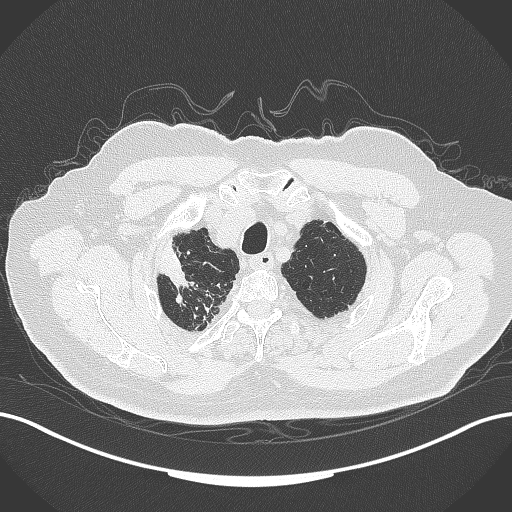
Chest CT, one axial slice; position 318 of 389 along the scan axis; reconstruction kernel B70f; lung window (W 1500 / L -600 HU); 512 × 512 image matrix. Patient: male, 72 years. From the clinical record (not read from this slice): clinical TNM (as recorded): T1a N0 M0.
Outlined on this slice (rectangle marked by the reading radiologist):
- lung tumour (recorded histology: squamous cell carcinoma): bounding box <155,235,195,294> (left, top, right, bottom; pixels)